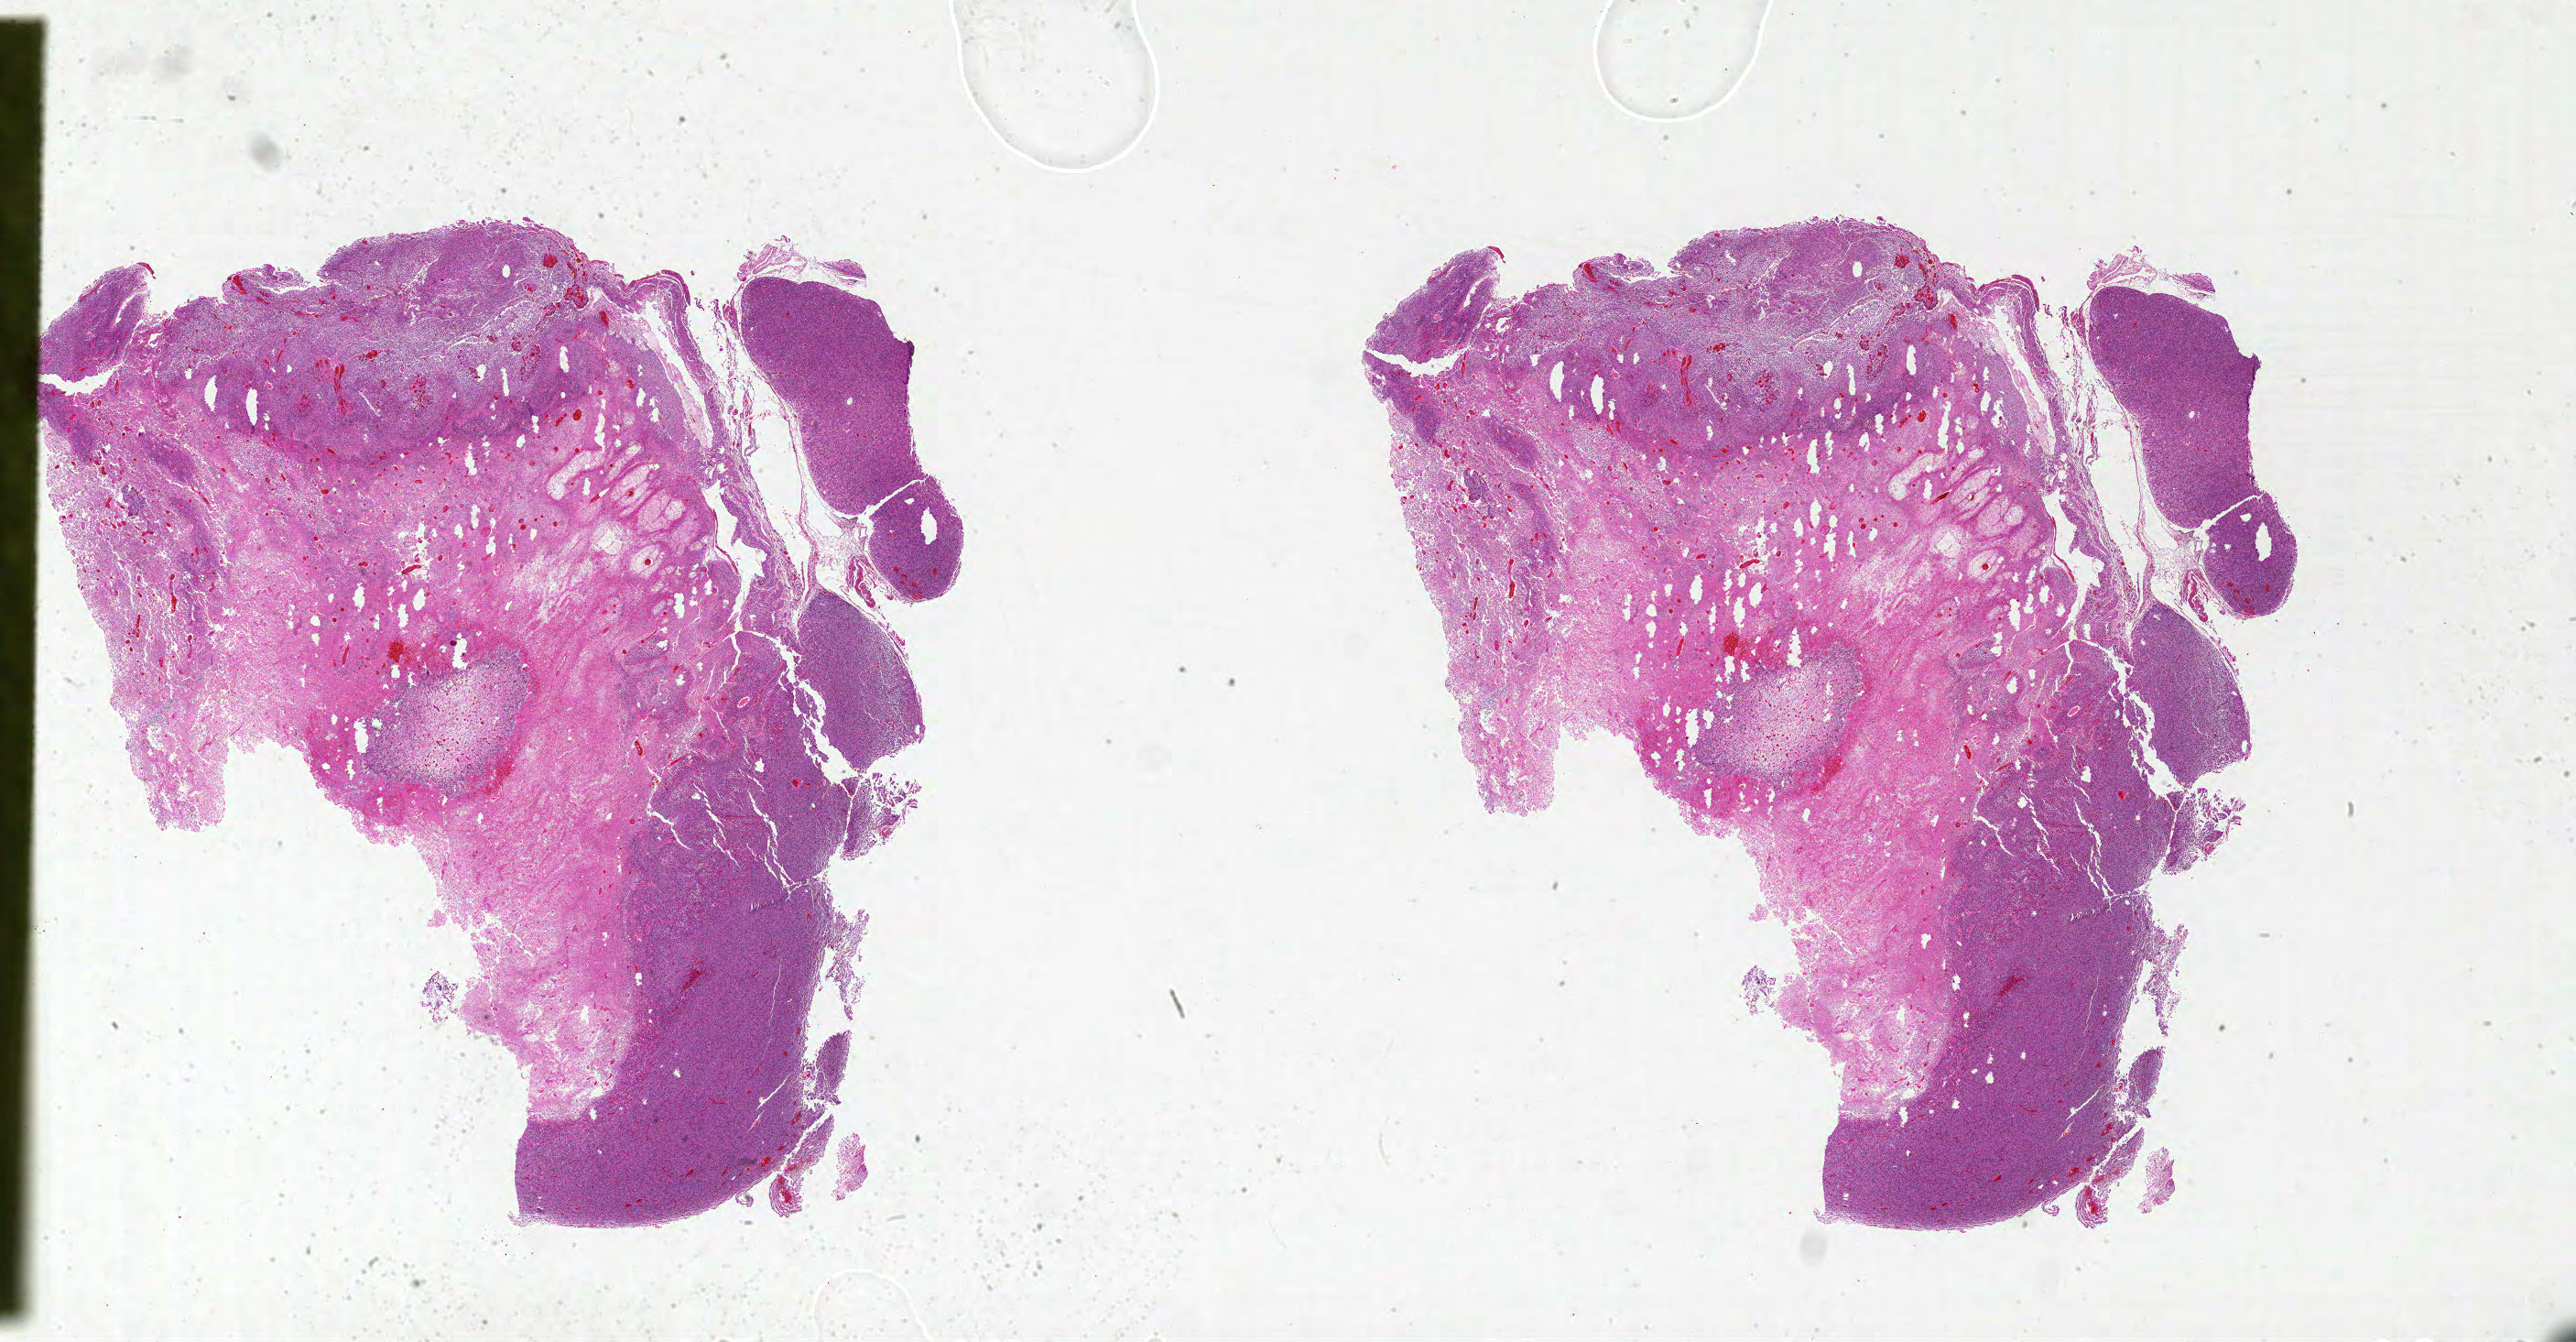
Whole-slide histology image, Hematoxylin and eosin (H&E) stained, whole scanned area (about 45.0 x 23.4 mm, slide scanned at 20x) shown as a low-resolution overview; formalin-fixed paraffin-embedded (FFPE) diagnostic section; sample: primary tumour, brain. Female, age 34 years at initial diagnosis.
Histologic diagnosis: Glioblastoma.